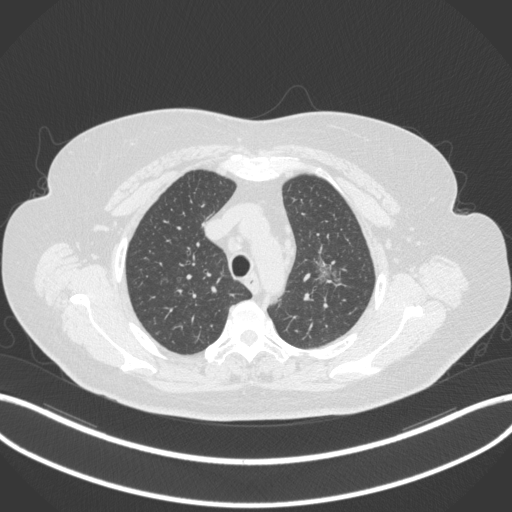
Chest CT, one axial slice. Slice 261 of 310 in the series (ordered by position). Lung window (W 1500 / L -600 HU). 512 × 512 image matrix, field of view 400 × 400 mm. Patient: female, 70 years. From the clinical record (not read from this slice): clinical TNM (as recorded): T1c N0 M0.
Annotated regions visible in this slice (rectangle marked by the reading radiologist):
- lung tumour (recorded histology: adenocarcinoma): bounding box <310,247,343,288> (left, top, right, bottom; pixels)